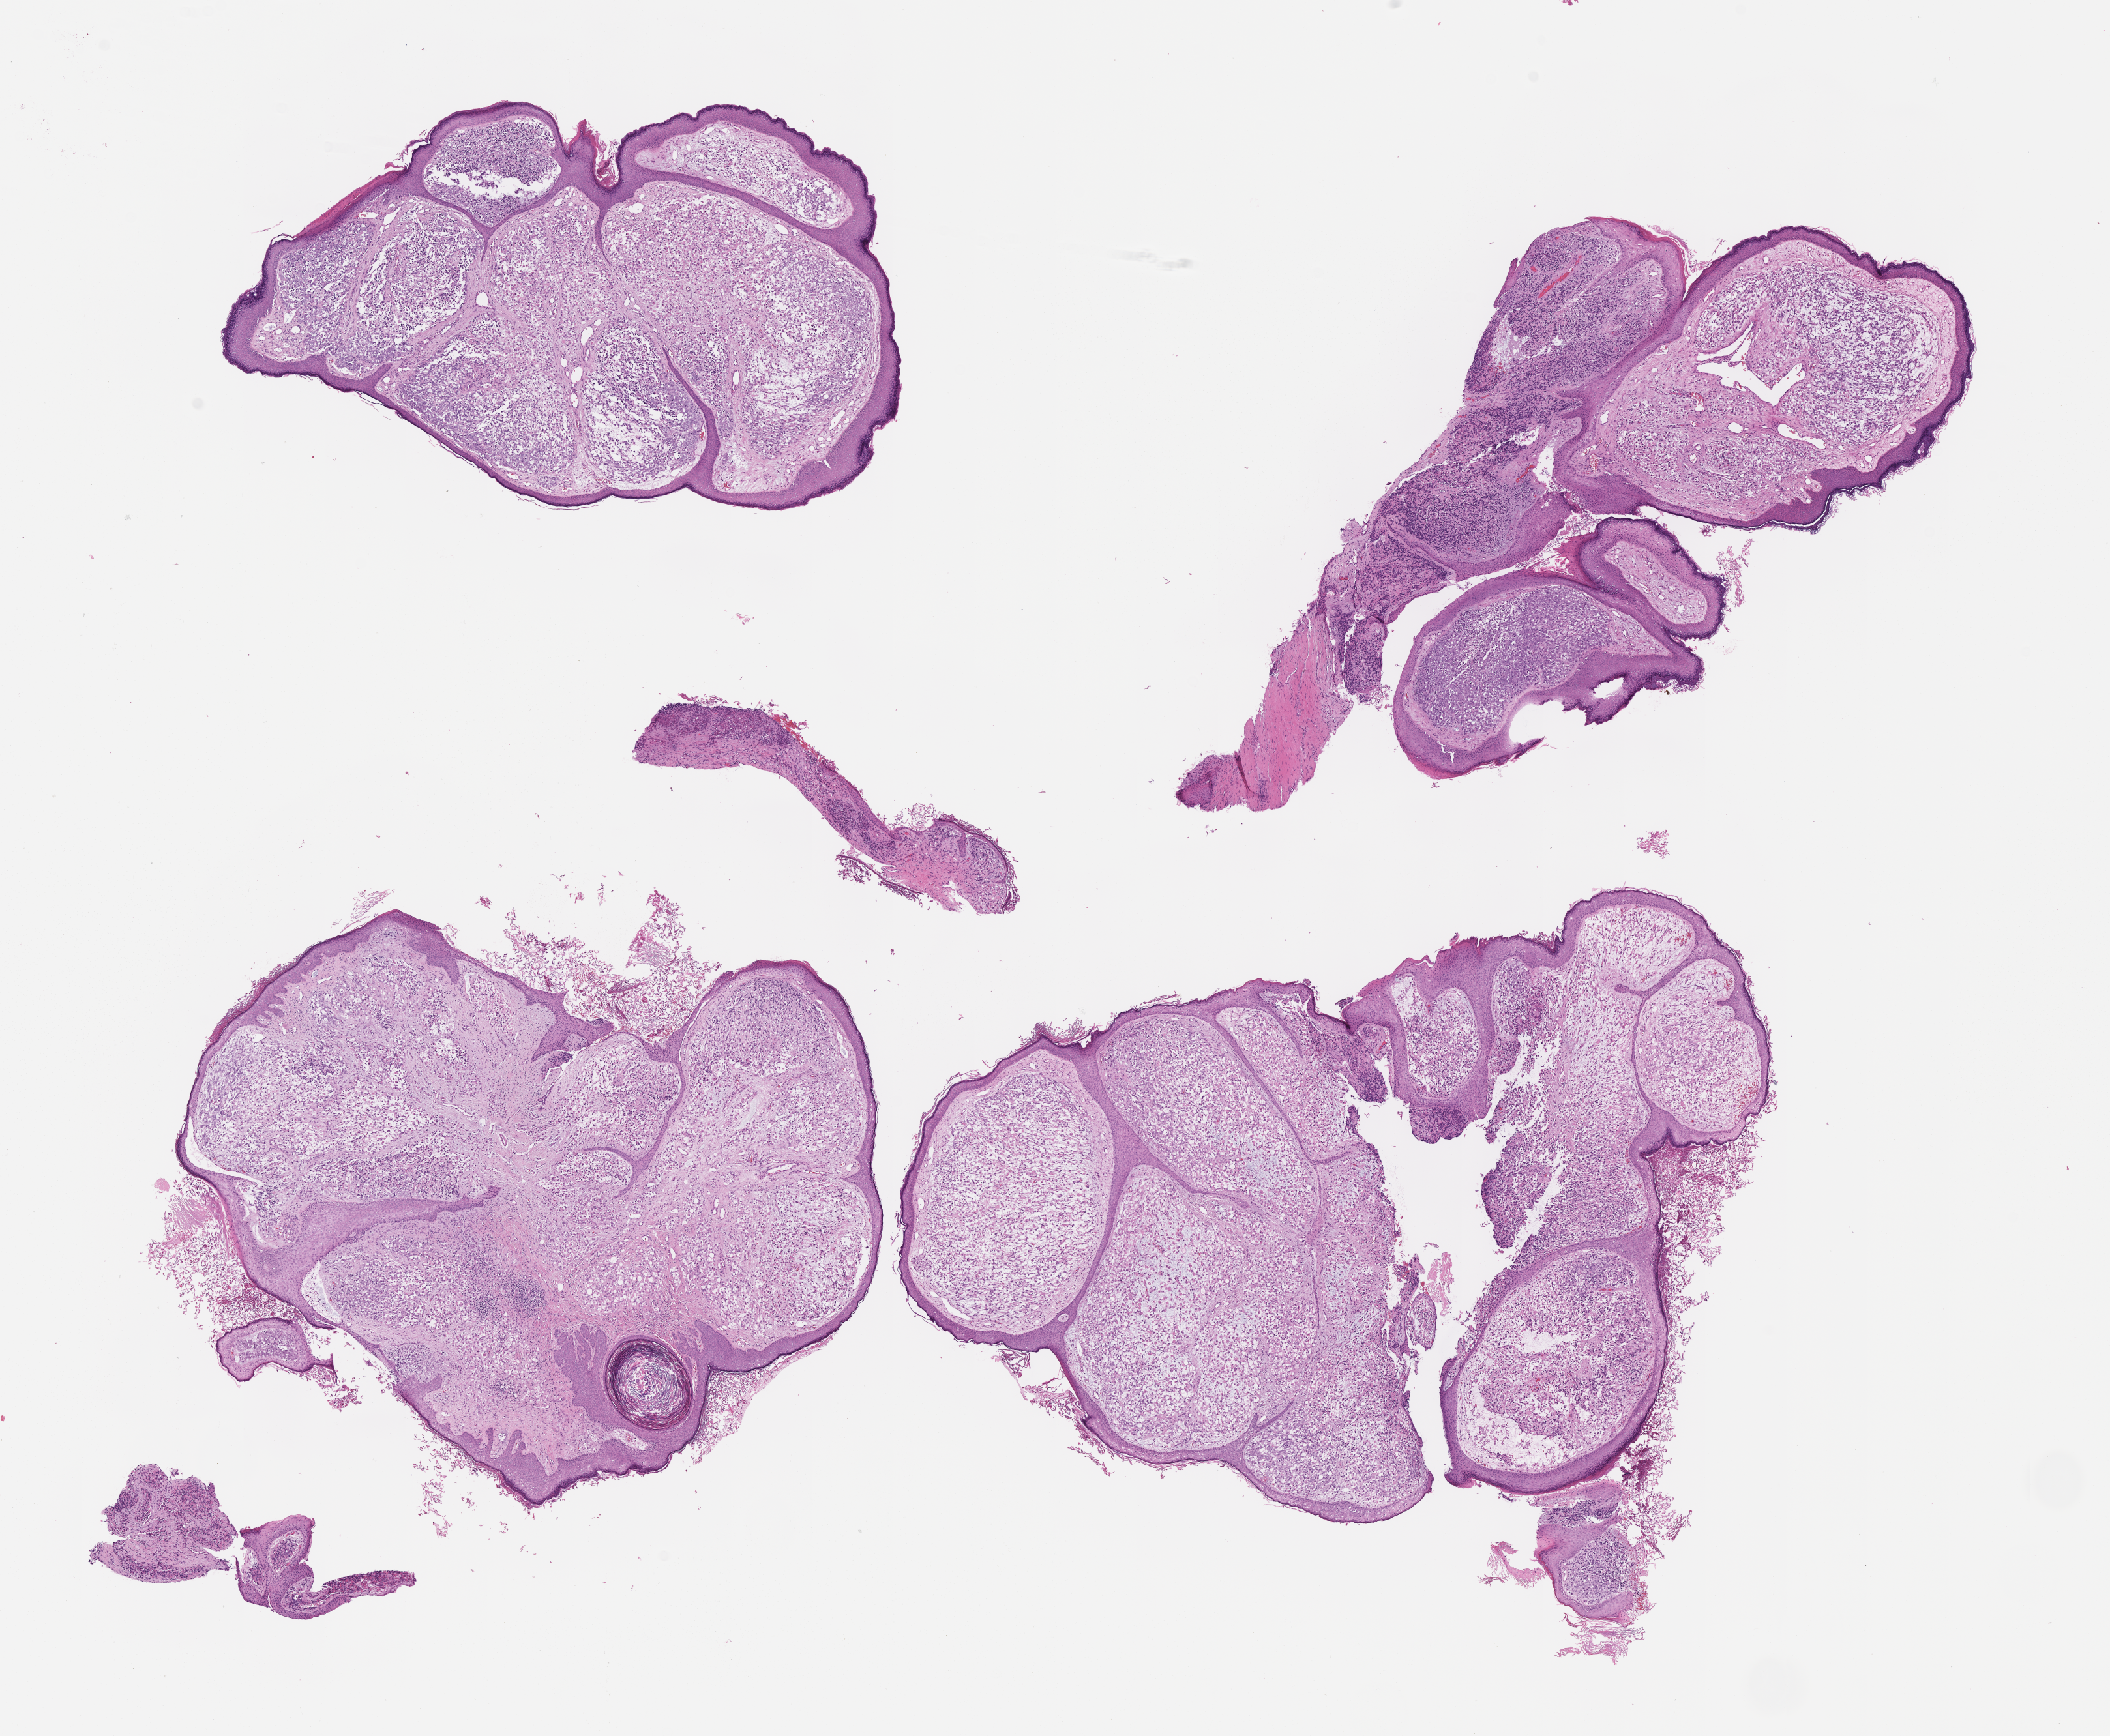
Whole-slide image, hematoxylin and eosin (H&E) stain of tumor tissue — low-resolution overview of the scanned area, about 13.1 x 10.8 mm, FFPE section. Patient: male, age 6.7 years at diagnosis.
Stage (as recorded): 1. Diagnosis: rhabdomyosarcoma; histological classification: embryonal rhabdomyosarcoma.